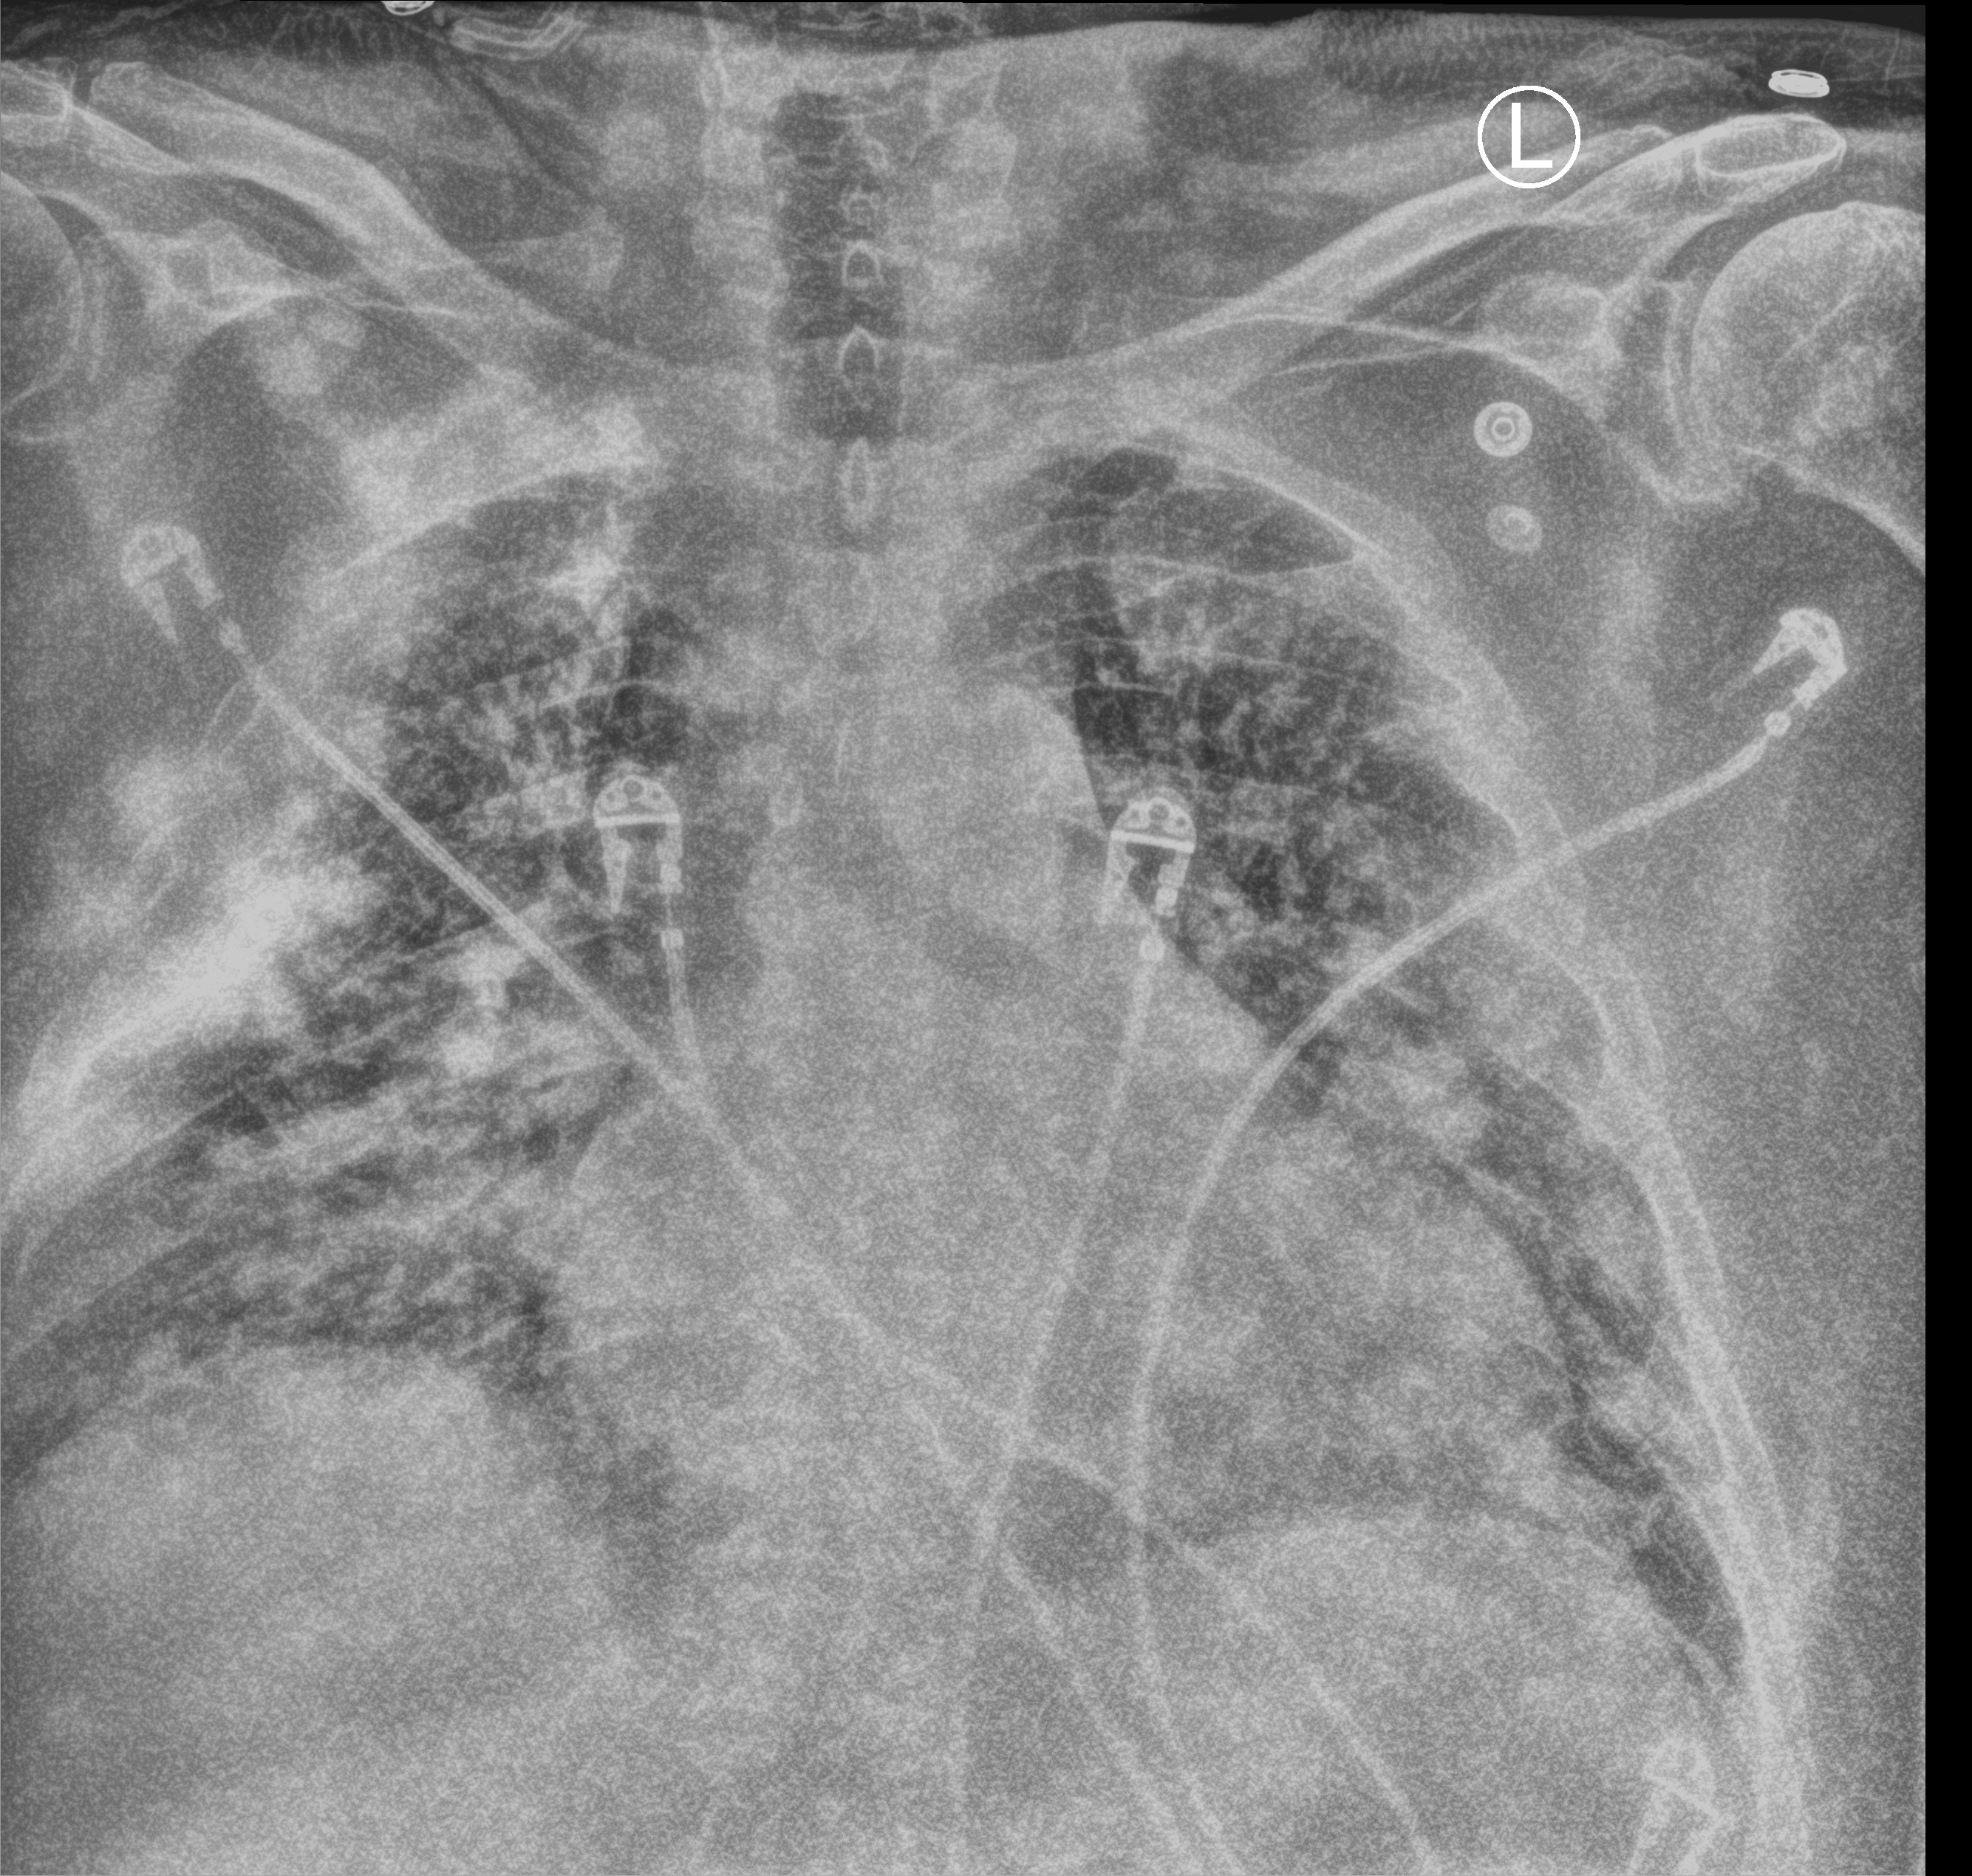
Portable chest radiograph, anteroposterior (AP) projection. Male patient hospitalised with COVID-19, age 60–74 years.
Admission-level facts for this patient (not findings on this image; timing relative to this image not recorded):
- length of hospital stay: 7 days
- mechanically ventilated during this hospital stay: yes